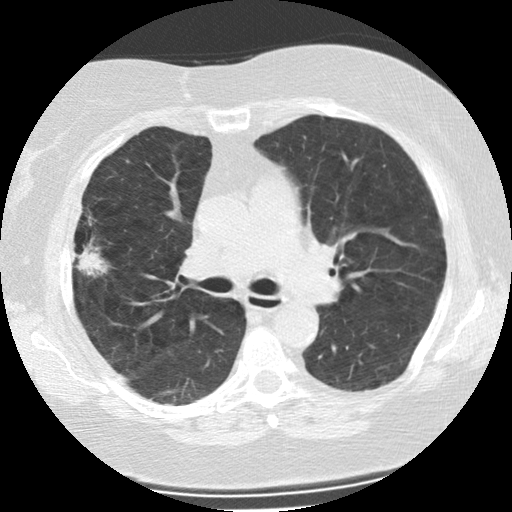
Chest CT (low-dose screening protocol), one axial image, second screening round (one year after baseline), lung window (W 1500 / L -600 HU), standard (soft-tissue) reconstruction kernel (STANDARD), slice 84 of 225 in the series, 512 × 512 image matrix. Female, age 73 years at enrolment. Former smoker at enrolment.
• Expert-annotated lung lesion, bounding box [x1, y1, x2, y2] px = [55, 213, 111, 285].
• The screening reader recorded 2 non-calcified nodules or masses ≥4 mm on this exam; which of them this box marks is not recorded.
• Official screen result: positive, change unspecified: nodule(s) >= 4 mm or enlarging nodule(s), mass(es), or other non-specific abnormalities suspicious for lung cancer.
• Participant outcome: lung cancer diagnosed 47 days after this screen — bronchiolo-alveolar adenocarcinoma, NOS, right upper lobe, moderately differentiated (G2), stage IIIB (AJCC 6th edition), 21 mm at pathology.